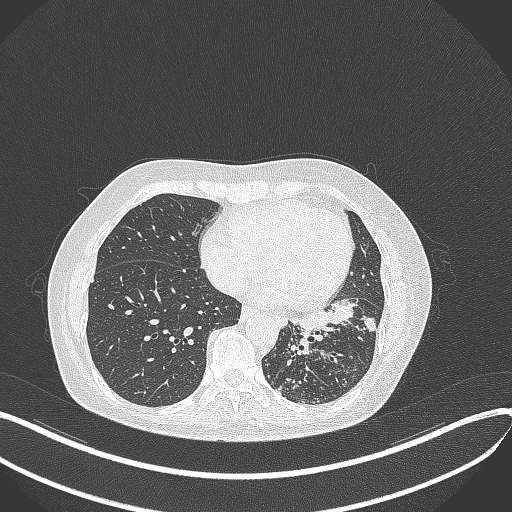
Chest CT, one axial slice. Slice 144 of 429 in the series (ordered by position). 100 kVp. Lung window (W 1500 / L -600 HU). 1 mm slice thickness. 512 × 512 image matrix, field of view 400 × 400 mm. Patient: female, 63 years. From the clinical record (not read from this slice): clinical TNM (as recorded): T1b N0 M0; histopathological grade: G2-3.
Outlined on this slice (rectangle marked by the reading radiologist):
- lung tumour (recorded histology: adenocarcinoma): bounding box (x1, y1, x2, y2) in pixels: (282, 297, 377, 340)